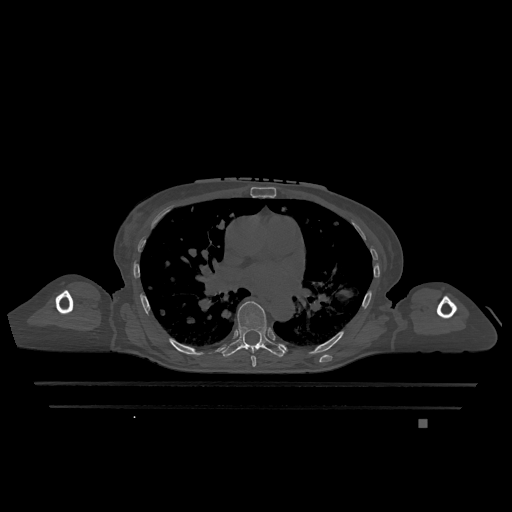
CT including the spine, one axial slice; position 751 of 1317 along the scan axis; bone window (W 1800 / L 400 HU); 512 × 512 image matrix. Female patient, age 74 years. From the clinical record (not read from this slice): primary cancer: lung; vertebrae with lytic lesions (as recorded): T1, T4, T5, T6, L4, L5.
Structures marked on this image (semi-automatically segmented with operator editing):
- T6 vertebra: bounding box [x1, y1, x2, y2] px = [251, 356, 256, 367]
- T7 vertebra: [220, 301, 286, 357]